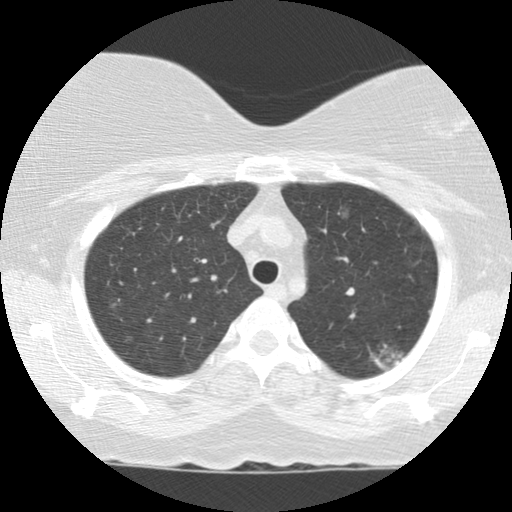
Low-dose screening chest CT, axial slice; baseline screening round; lung window (W 1500 / L -600 HU); 2.5 mm slice thickness; standard (soft-tissue) reconstruction kernel (STANDARD); slice 24 of 123 in the series. Female participant, aged 56 years at enrolment. Current smoker at enrolment.
Expert-annotated lung lesion, bounding box [x1, y1, x2, y2] px = [356, 318, 418, 383]. The screening reader recorded 4 non-calcified nodules or masses ≥4 mm on this exam; which of them this box marks is not recorded. Lung cancer was diagnosed 798 days after this screen: adenocarcinoma, NOS, left upper lobe, moderately differentiated (G2), stage IA (AJCC 6th edition), 10 mm at pathology.